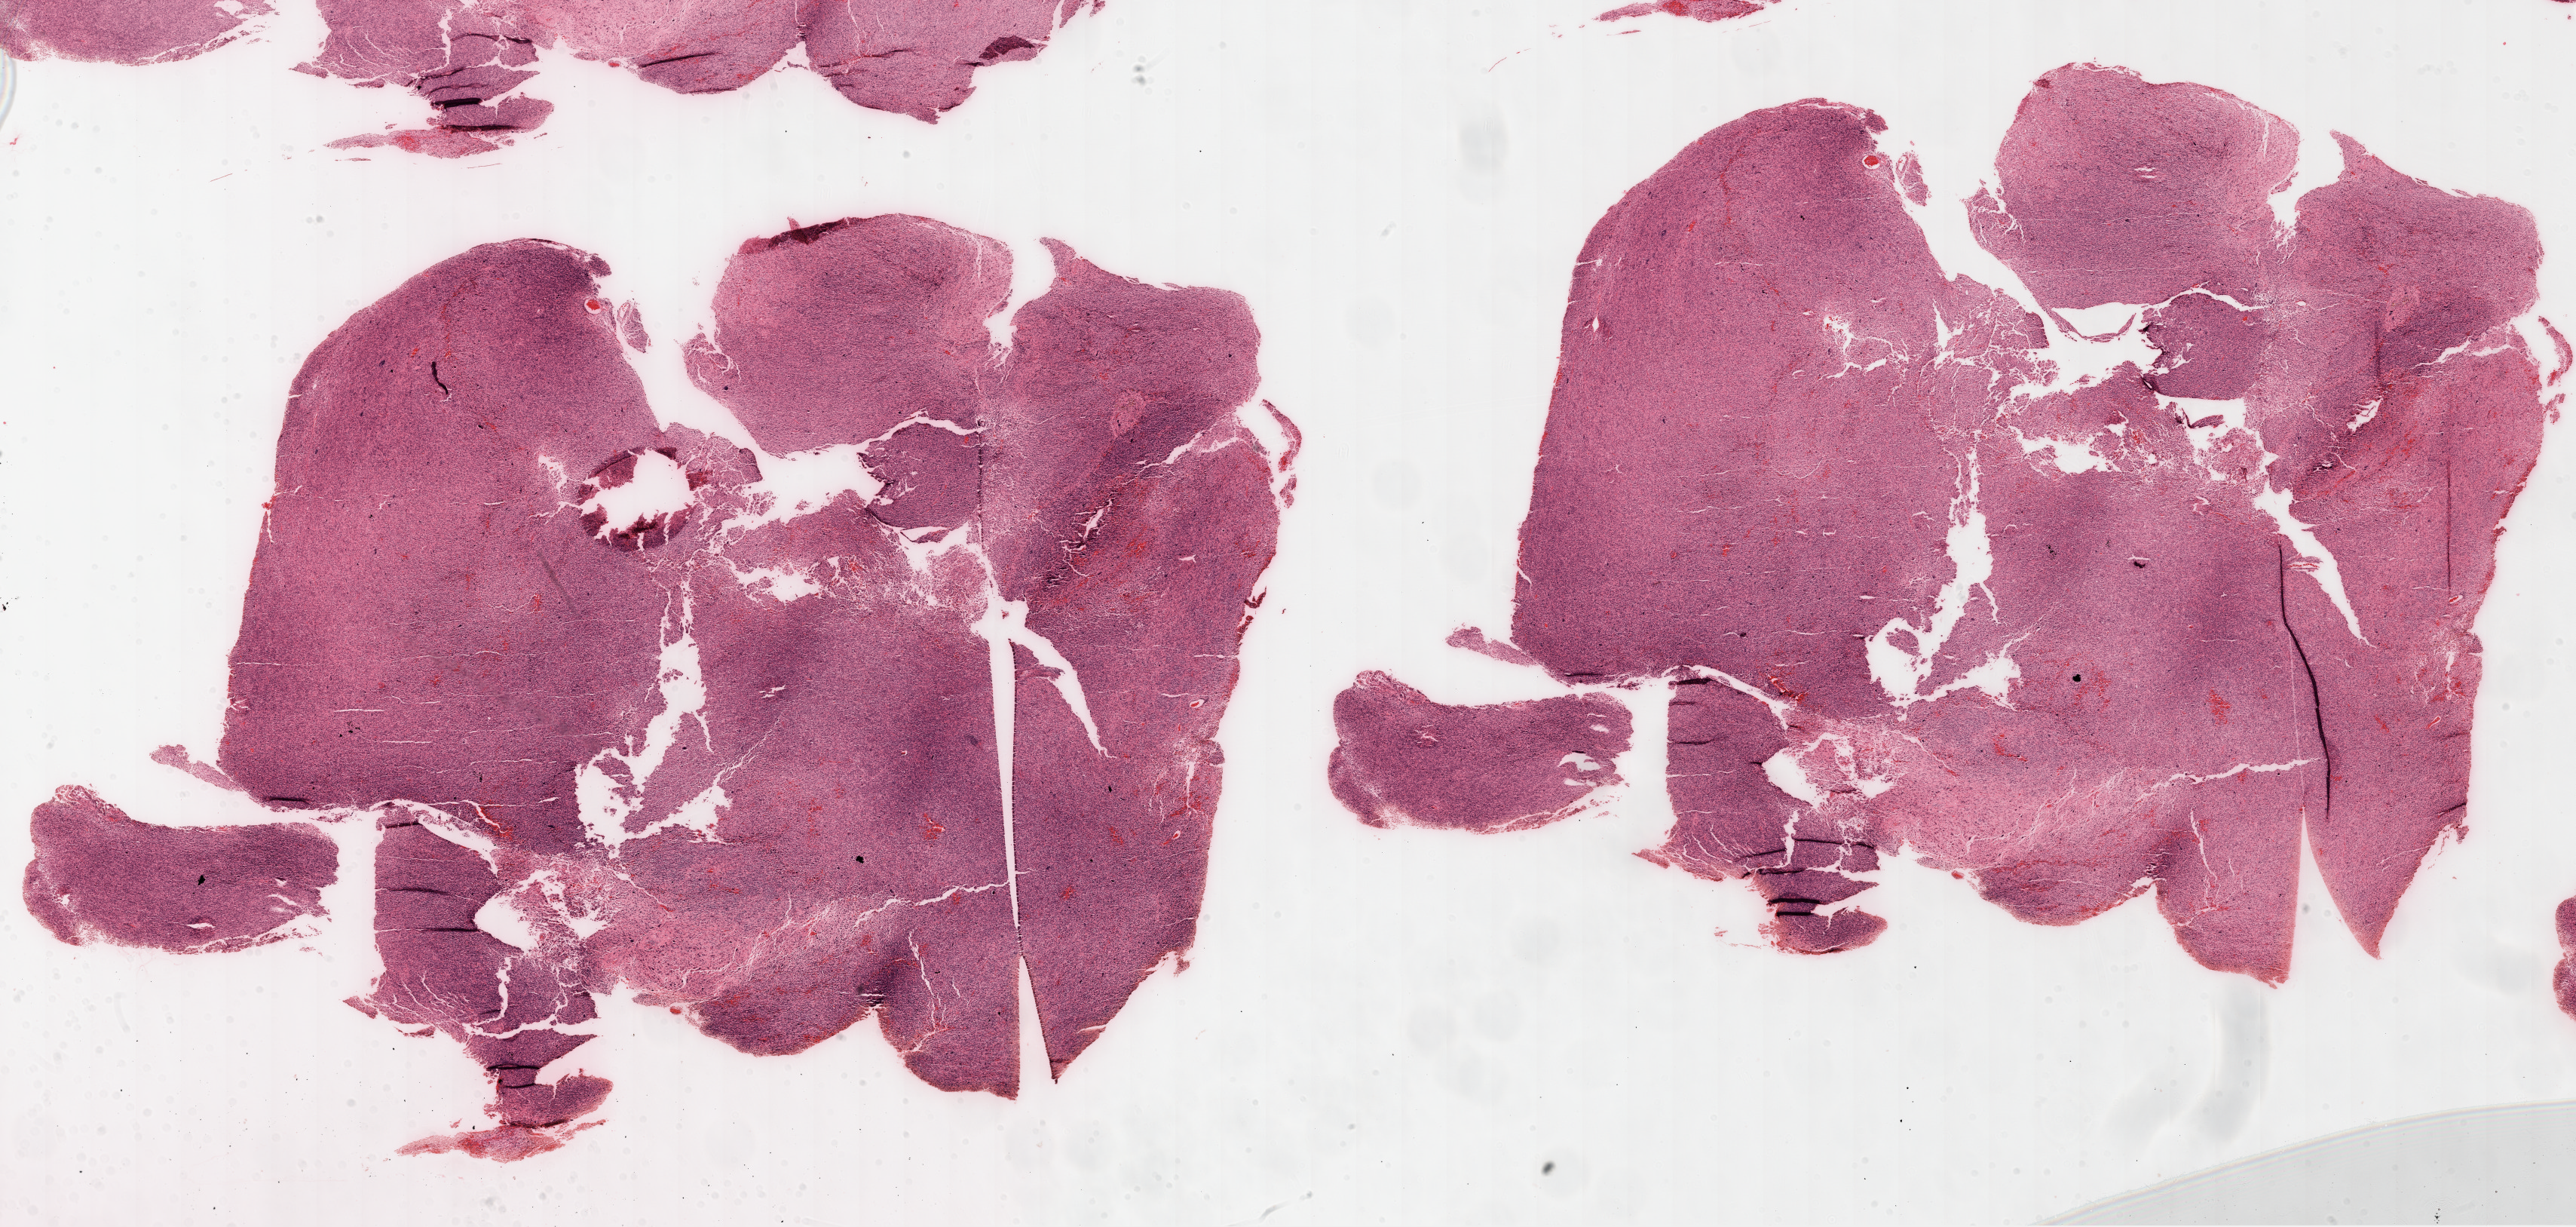
Hematoxylin and eosin (H&E) stained whole-slide image — whole scanned area (about 27.6 x 13.1 mm, slide scanned at 20x) shown as a low-resolution overview. Formalin-fixed paraffin-embedded (FFPE) diagnostic section. Primary tumour sample from the brain. Patient: male, age at initial diagnosis 63 years.
Diagnosis: Glioblastoma.